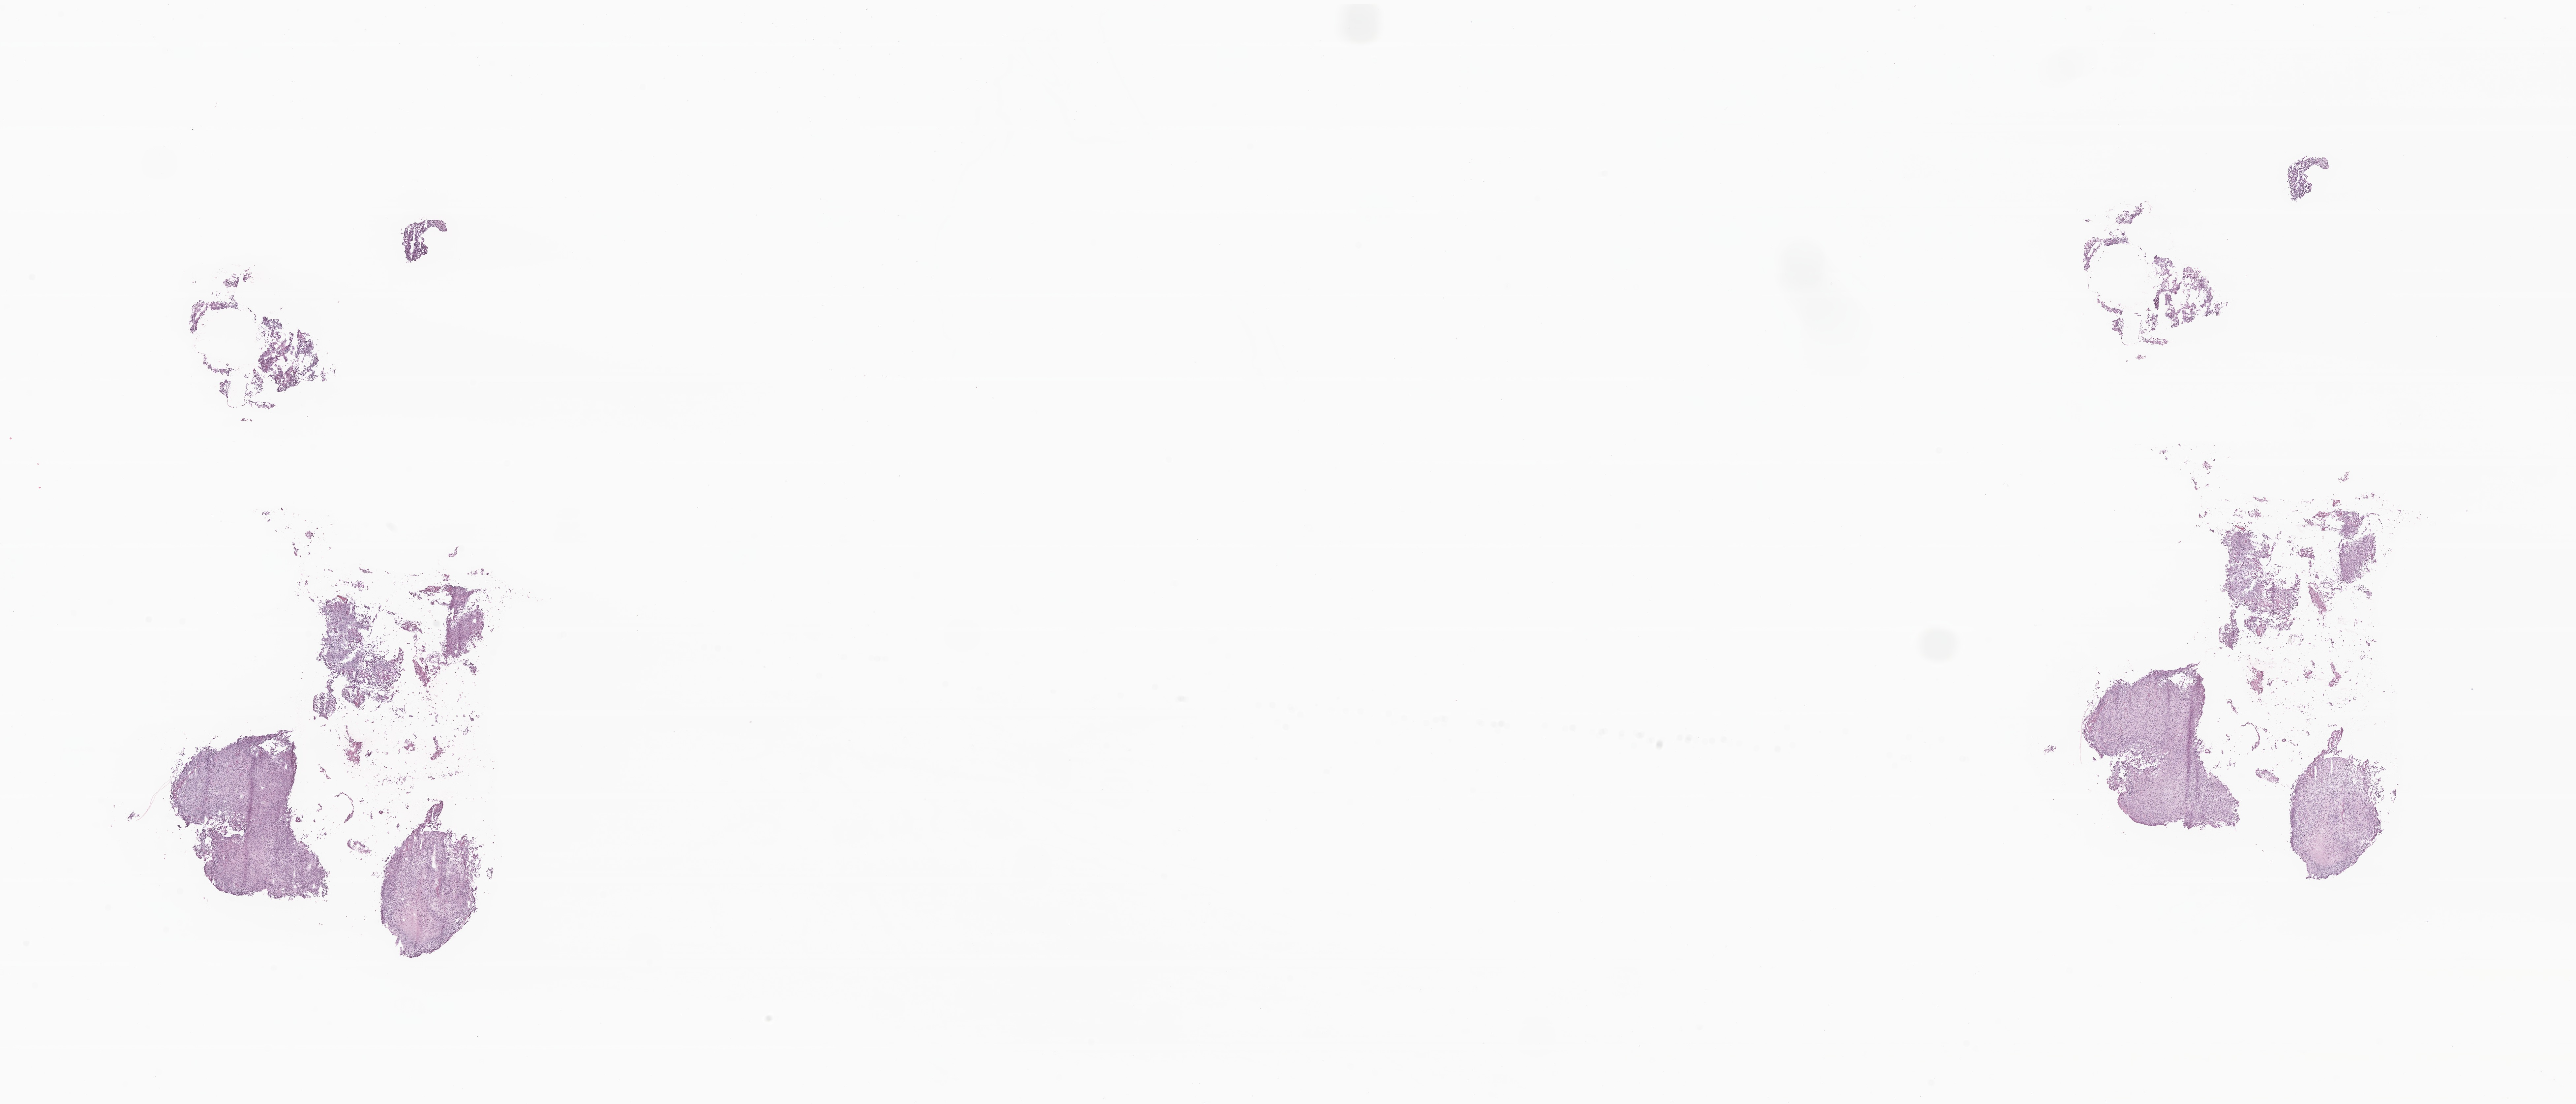
Digitized hematoxylin and eosin (H&E)-stained section of tumor tissue from the brain — whole scanned area (about 32.9 x 14.1 mm) shown as a low-resolution overview; frozen section (OCT-embedded). Female patient, age 122 months (10 years 2 months).
Diagnosis (ICD-O-3 morphology term): Astrocytoma, NOS.